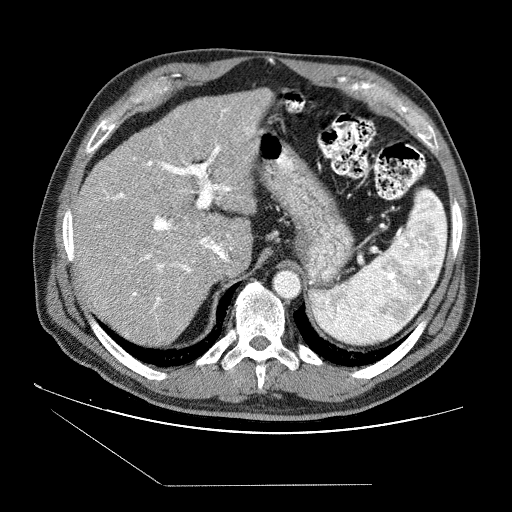
Contrast-enhanced abdominal CT (liver protocol), one axial slice; position 57 of 87 along the scan axis; soft-tissue window (W 400 / L 40 HU); 2.5 mm slice thickness; 512 × 512 image matrix, field of view 400 × 400 mm. From the clinical record (not read from this slice): diagnosis: hepatocellular carcinoma (patient treated with transarterial chemoembolisation; whether this scan precedes or follows treatment is not stated here); TNM stage (as recorded): Stage-II; Child-Pugh class: B; tumour differentiation: no biopsy.
Outlined on this slice (semi-automatic segmentation, software-assisted and operator-edited):
- liver parenchyma outside the tumour (the mass and vessels are separate outlines, so this box may not span the whole liver): bounding box <72,88,272,344> (left, top, right, bottom; pixels)
- liver vessels: <98,108,254,336>